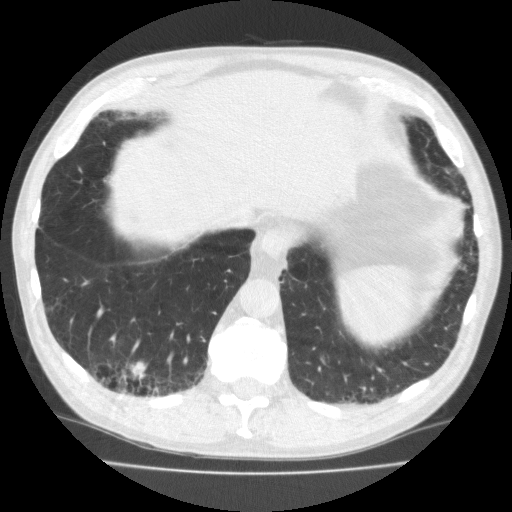
Low-dose screening chest CT, one axial slice; slice 52 of 195 in the series (ordered by position); reconstruction kernel FC10; 120 kVp; lung window (W 1500 / L -600 HU); 512 × 512 image matrix.
Annotated regions visible in this slice (expert manual segmentation):
- lesion 1 (tumor, lower lobe of right lung): box from (x=126, y=361) to (x=147, y=385) px